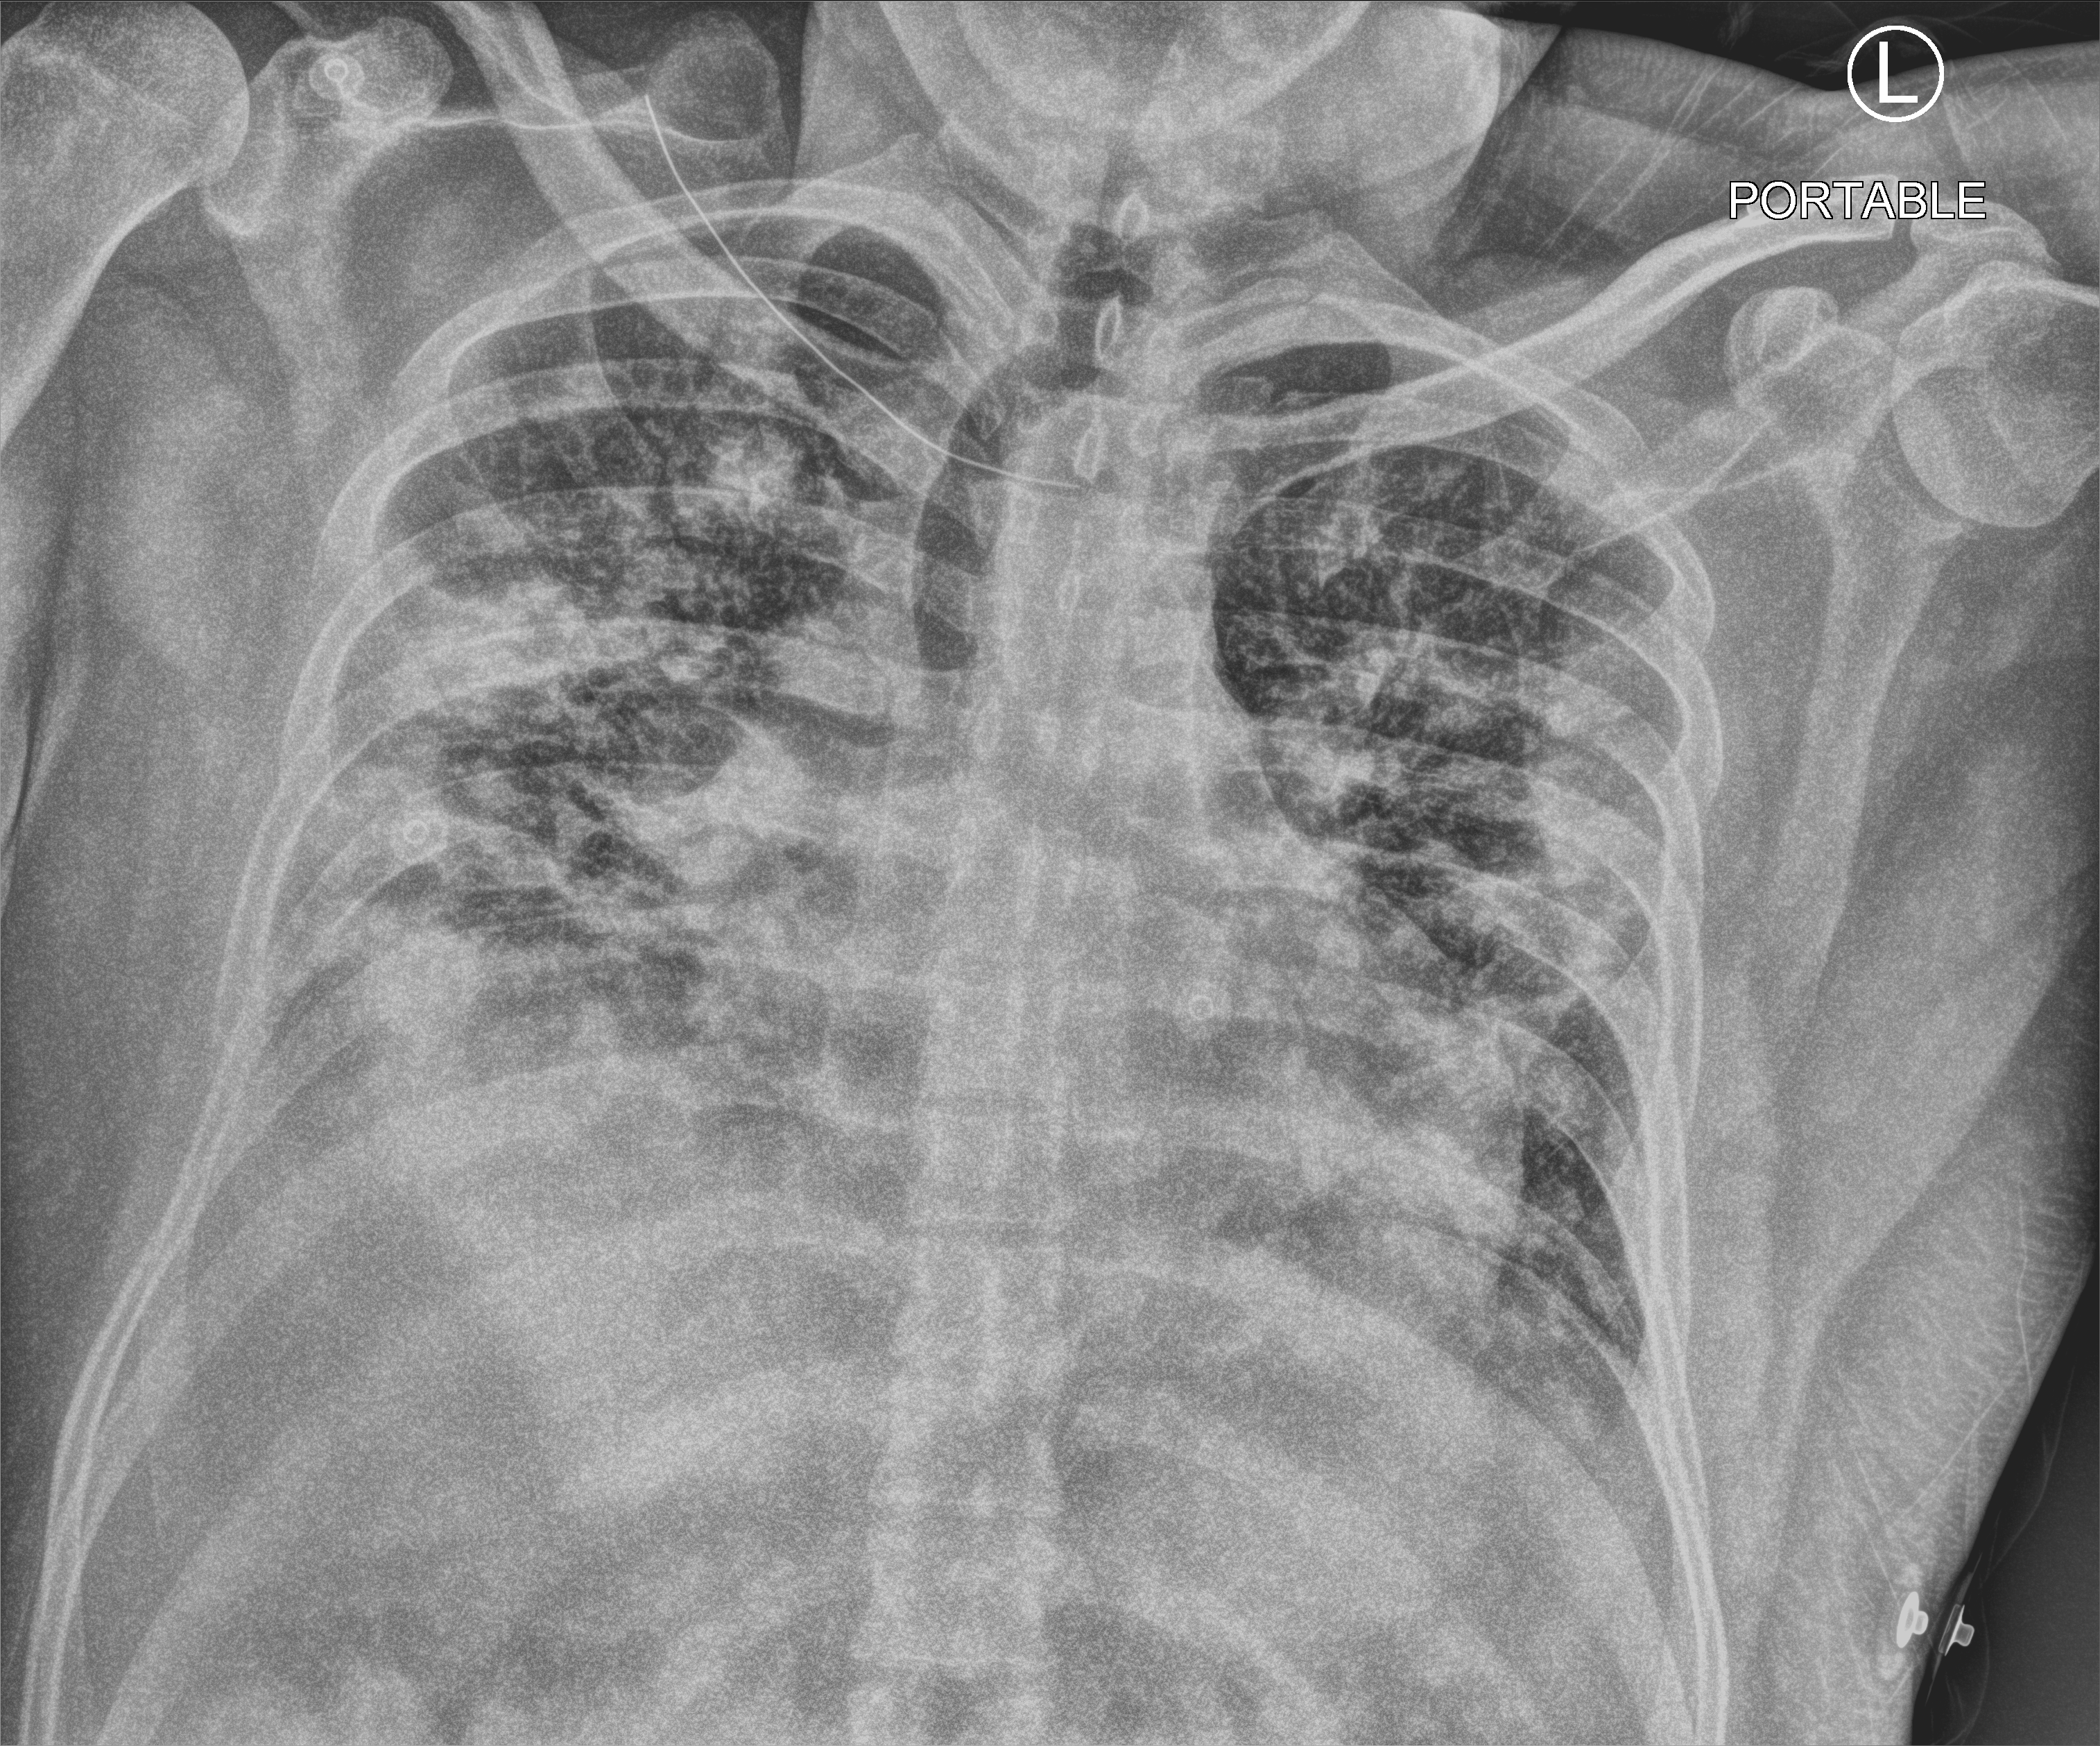
Bedside chest radiograph (computed radiography). Male patient hospitalised with COVID-19, age 18–59 years.
From the hospital-stay record, not from the radiograph (when in the stay this image was taken is not recorded):
- diabetes (admission record): no